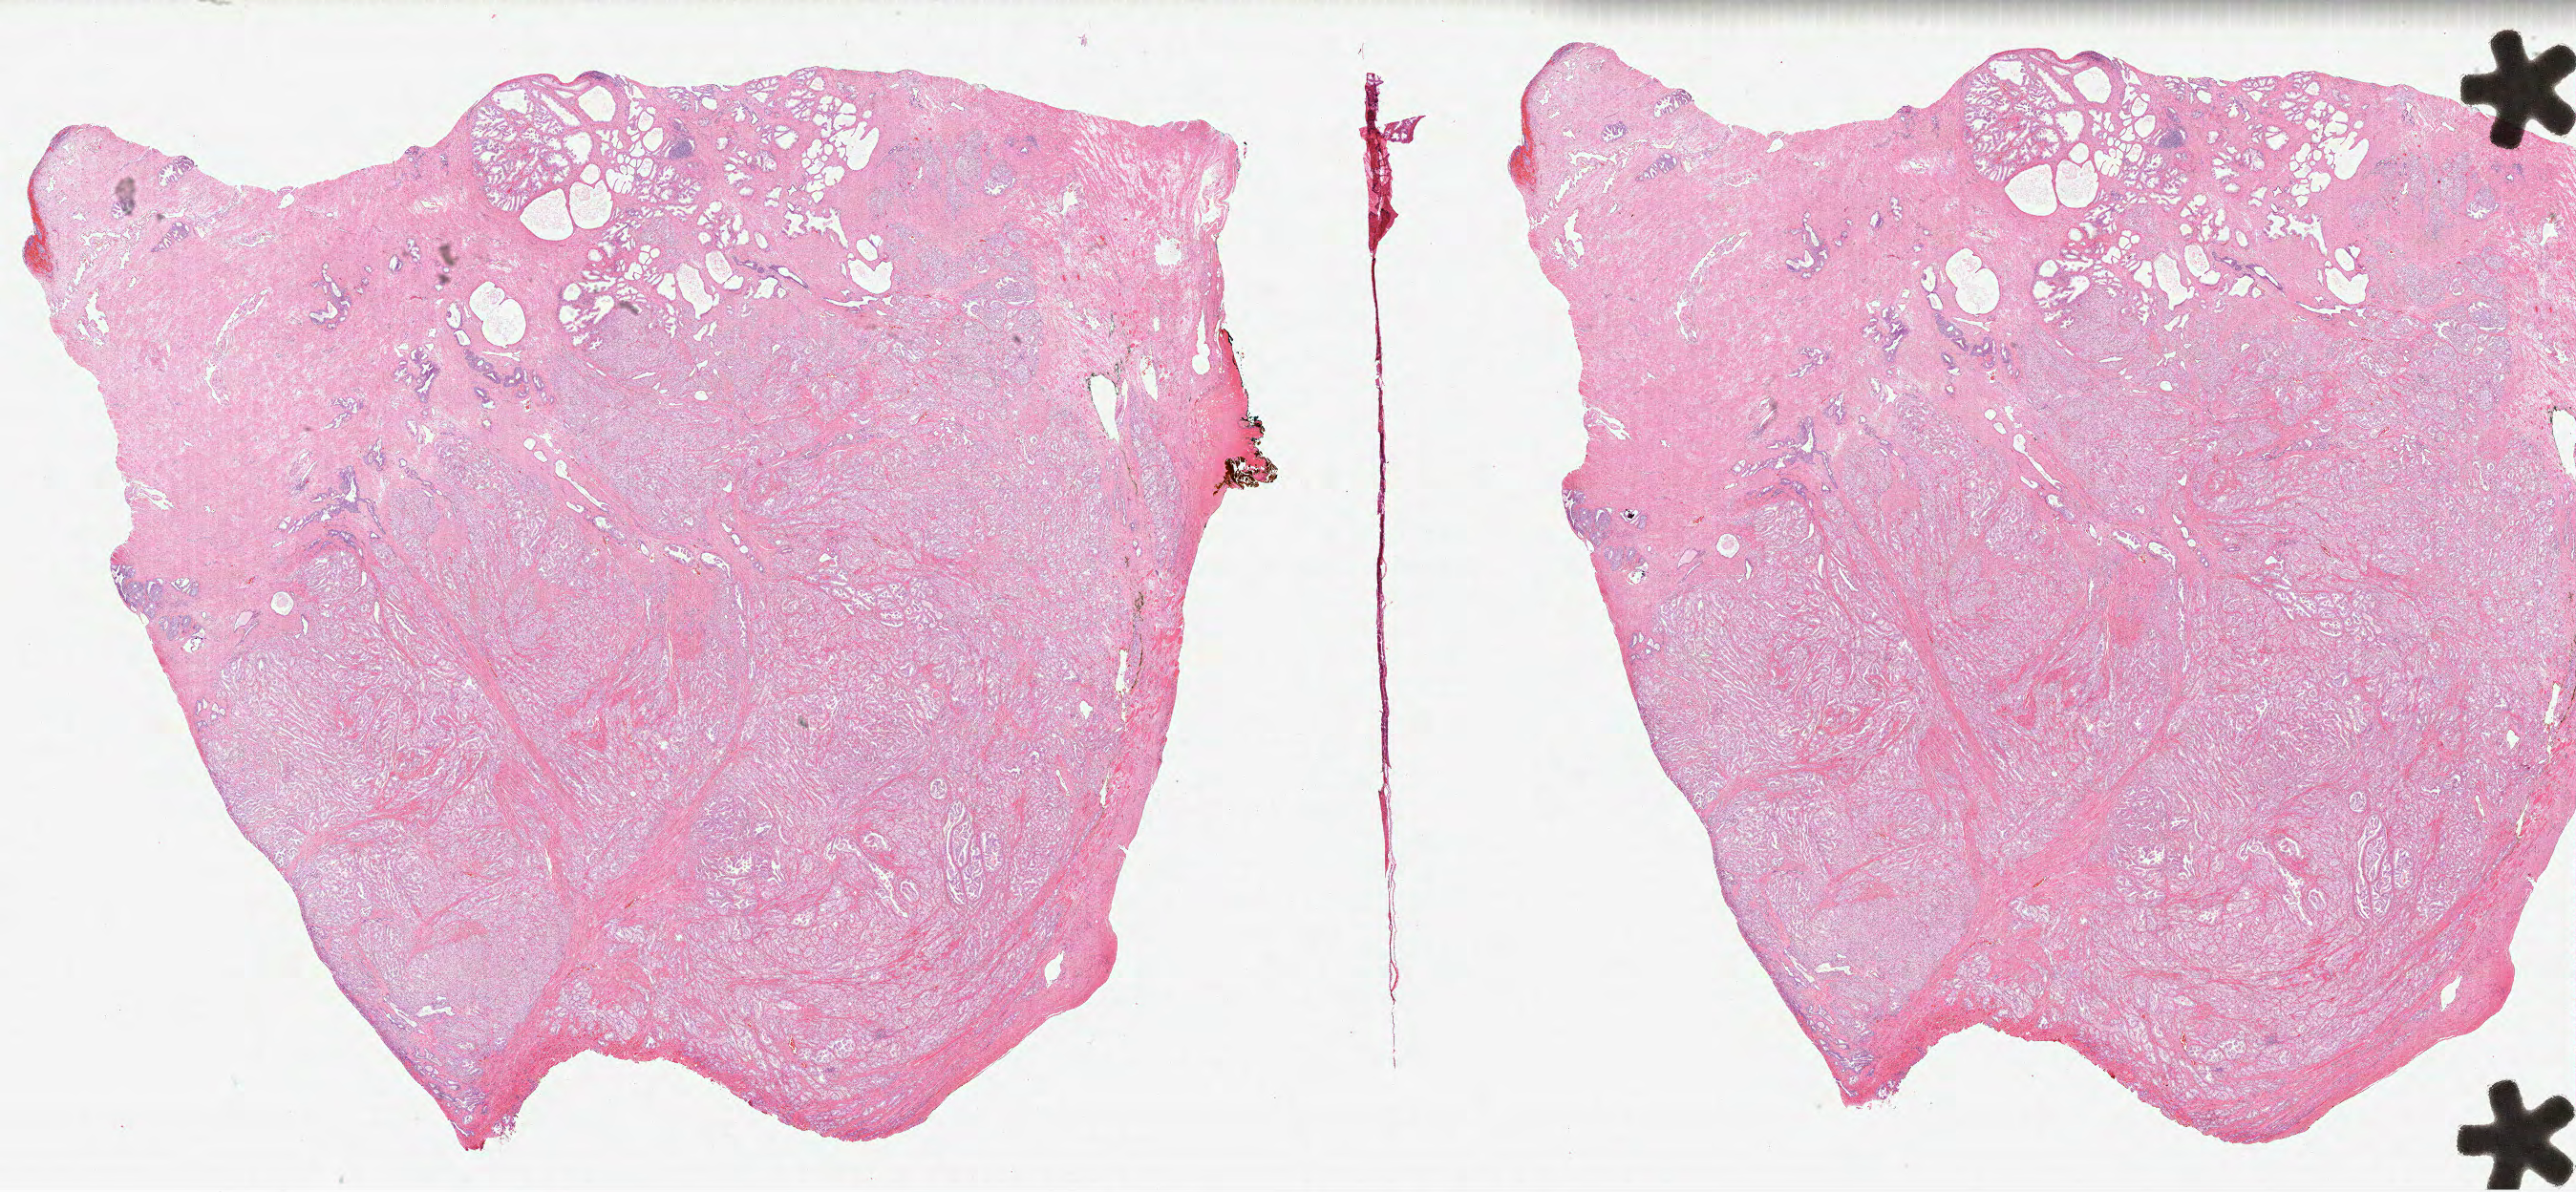
Whole-slide histology image, H&E-stained — a low-resolution overview of the entire scanned area, about 43.5 x 20.1 mm (from a 40x scan). FFPE section. Prostate, primary tumour sample. Male, age 61 years at initial diagnosis. Gleason score: 7 (4+3).
* diagnosis: Acinar cell carcinoma (prostate gland)